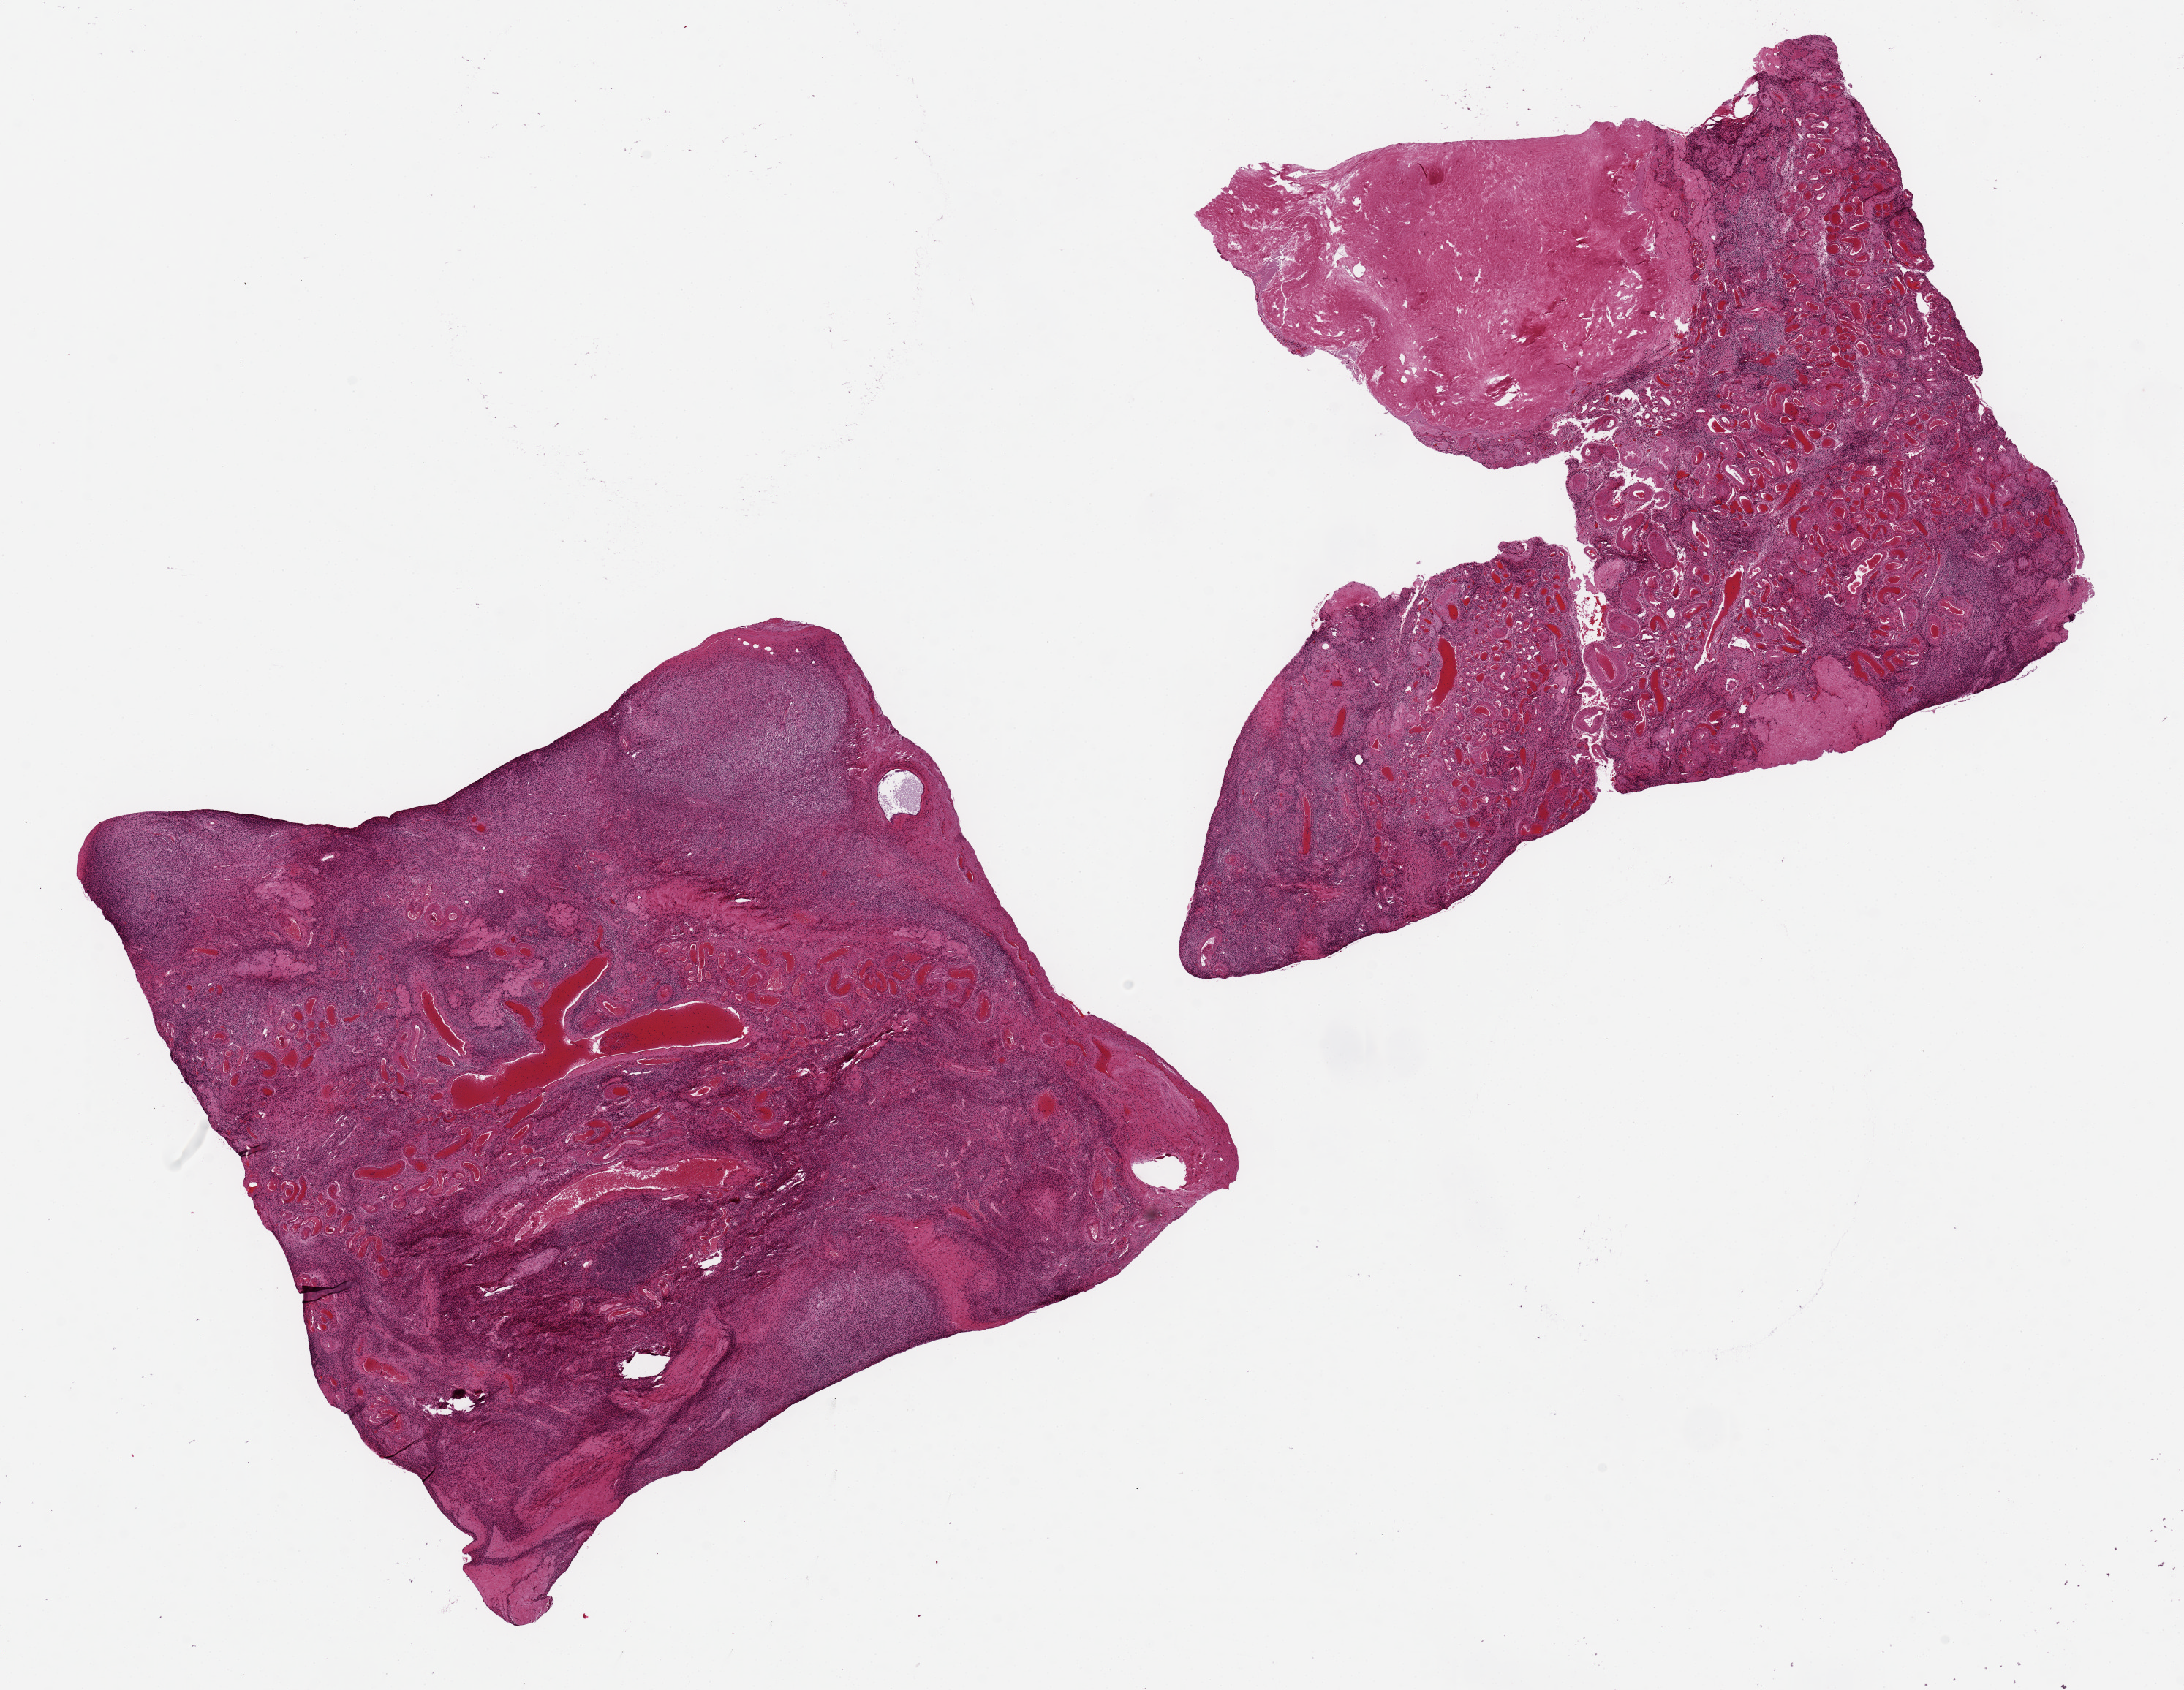
H&E whole-slide image — shown as a low-resolution overview of the whole scanned area (about 23.6 x 18.3 mm, acquisition: 20x scan); PAXgene-fixed paraffin-embedded (PFPE) section; sampled site (target tissue): ovary; tissue donor sample. Donor sex: female.
Pathologist's review note for this sample: 2 aliquots, ~10x8mm, post menopausal atrophy.